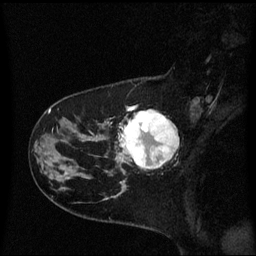
Breast MRI (dynamic contrast-enhanced), one sagittal slice. Position 17 of 60 along the scan axis. Dynamic contrast-enhanced series, image 2 of 3 at this slice position (ordered by acquisition). 1.5 T. TE 4.2 ms, TR 8.4 ms. 2 mm slice thickness. 256 × 256 image matrix, field of view 220 × 220 mm. Patient: female, 41 years. From the clinical record (not read from this slice): setting: breast cancer imaged before/during neoadjuvant chemotherapy; receptor status: triple-negative.
Annotated regions visible in this slice (semi-automatic segmentation, software-assisted and operator-edited):
- analysis volume of interest (the breast-tissue region the enhancement analysis was run in; not a lesion): bounding box [x1, y1, x2, y2] px = [116, 106, 179, 175]
- tumour enhancement mask (voxels above the 70 % enhancement threshold inside the analysis volume of interest): [120, 110, 179, 169]